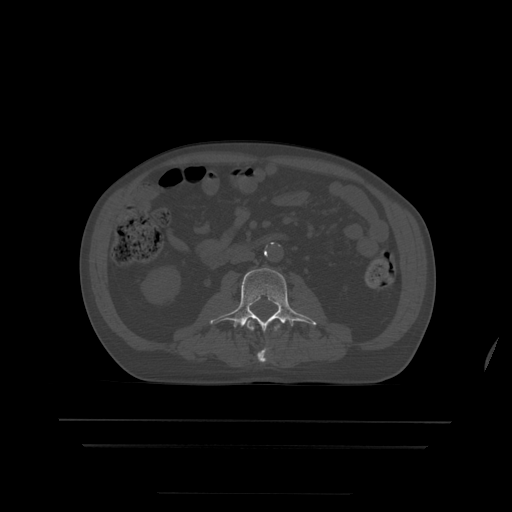
CT including the spine, one axial slice. Position 123 of 522 along the scan axis. Bone window (W 1800 / L 400 HU). 1.25 mm slice thickness. 512 × 512 image matrix, field of view 436 × 436 mm. Patient age 68 years. Case-level facts recorded for this patient, not image findings: primary cancer: urothelial.
Annotated regions visible in this slice (semi-automatically segmented with operator editing):
- L2 vertebra: bounding box <243,321,280,363> (left, top, right, bottom; pixels)
- L3 vertebra: <210,268,317,332>